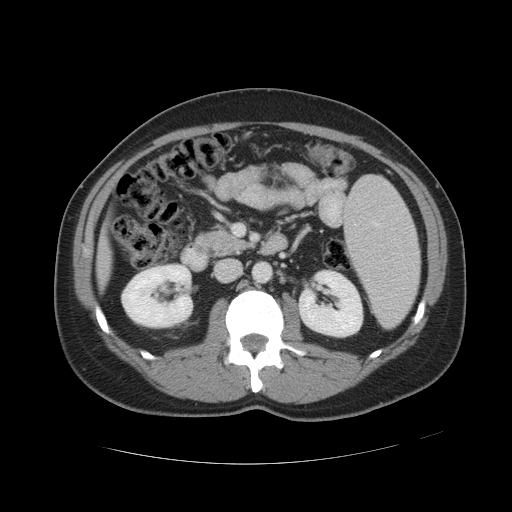
Contrast-enhanced abdominal CT, one axial slice; position 20 of 49 along the scan axis; reconstruction kernel STANDARD; 120 kVp; intravenous contrast given; soft-tissue window (W 400 / L 40 HU); 5 mm slice thickness; 512 × 512 image matrix, field of view 422 × 422 mm. Male patient, age 42 years. From the clinical record (not read from this slice): diagnosis: colorectal cancer liver metastases, imaged before liver resection; multiple liver metastases: yes; largest metastasis: 2.8 cm.
Annotated regions visible in this slice (manually delineated by an expert):
- liver: bounding box <103,243,110,272> (left, top, right, bottom; pixels)
- planned liver remnant (the part of the liver to remain after resection): <103,243,110,272>